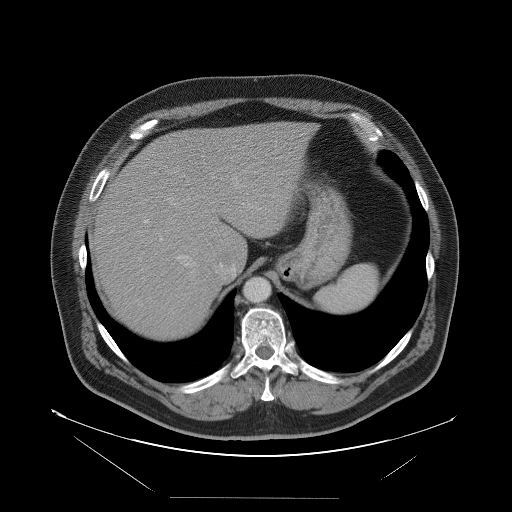
Contrast-enhanced abdominal CT, one axial slice. Position 77 of 114 along the scan axis. 120 kVp. Intravenous contrast given. Soft-tissue window (W 400 / L 40 HU). 5 mm slice thickness. 512 × 512 image matrix, field of view 500 × 500 mm. Male patient, age 61 years. Case-level facts recorded for this patient, not image findings: diagnosis: colorectal cancer liver metastases, imaged before liver resection; multiple liver metastases: no; largest metastasis: 6.5 cm; disease in both lobes: yes.
Outlined on this slice (outlined manually by an expert reader):
- hepatic veins: bounding box (x1, y1, x2, y2) in pixels: (166, 176, 271, 279)
- liver: (91, 124, 313, 340)
- planned liver remnant (the part of the liver to remain after resection): (147, 123, 313, 268)
- portal vein (with intrahepatic branches): (143, 219, 163, 241)